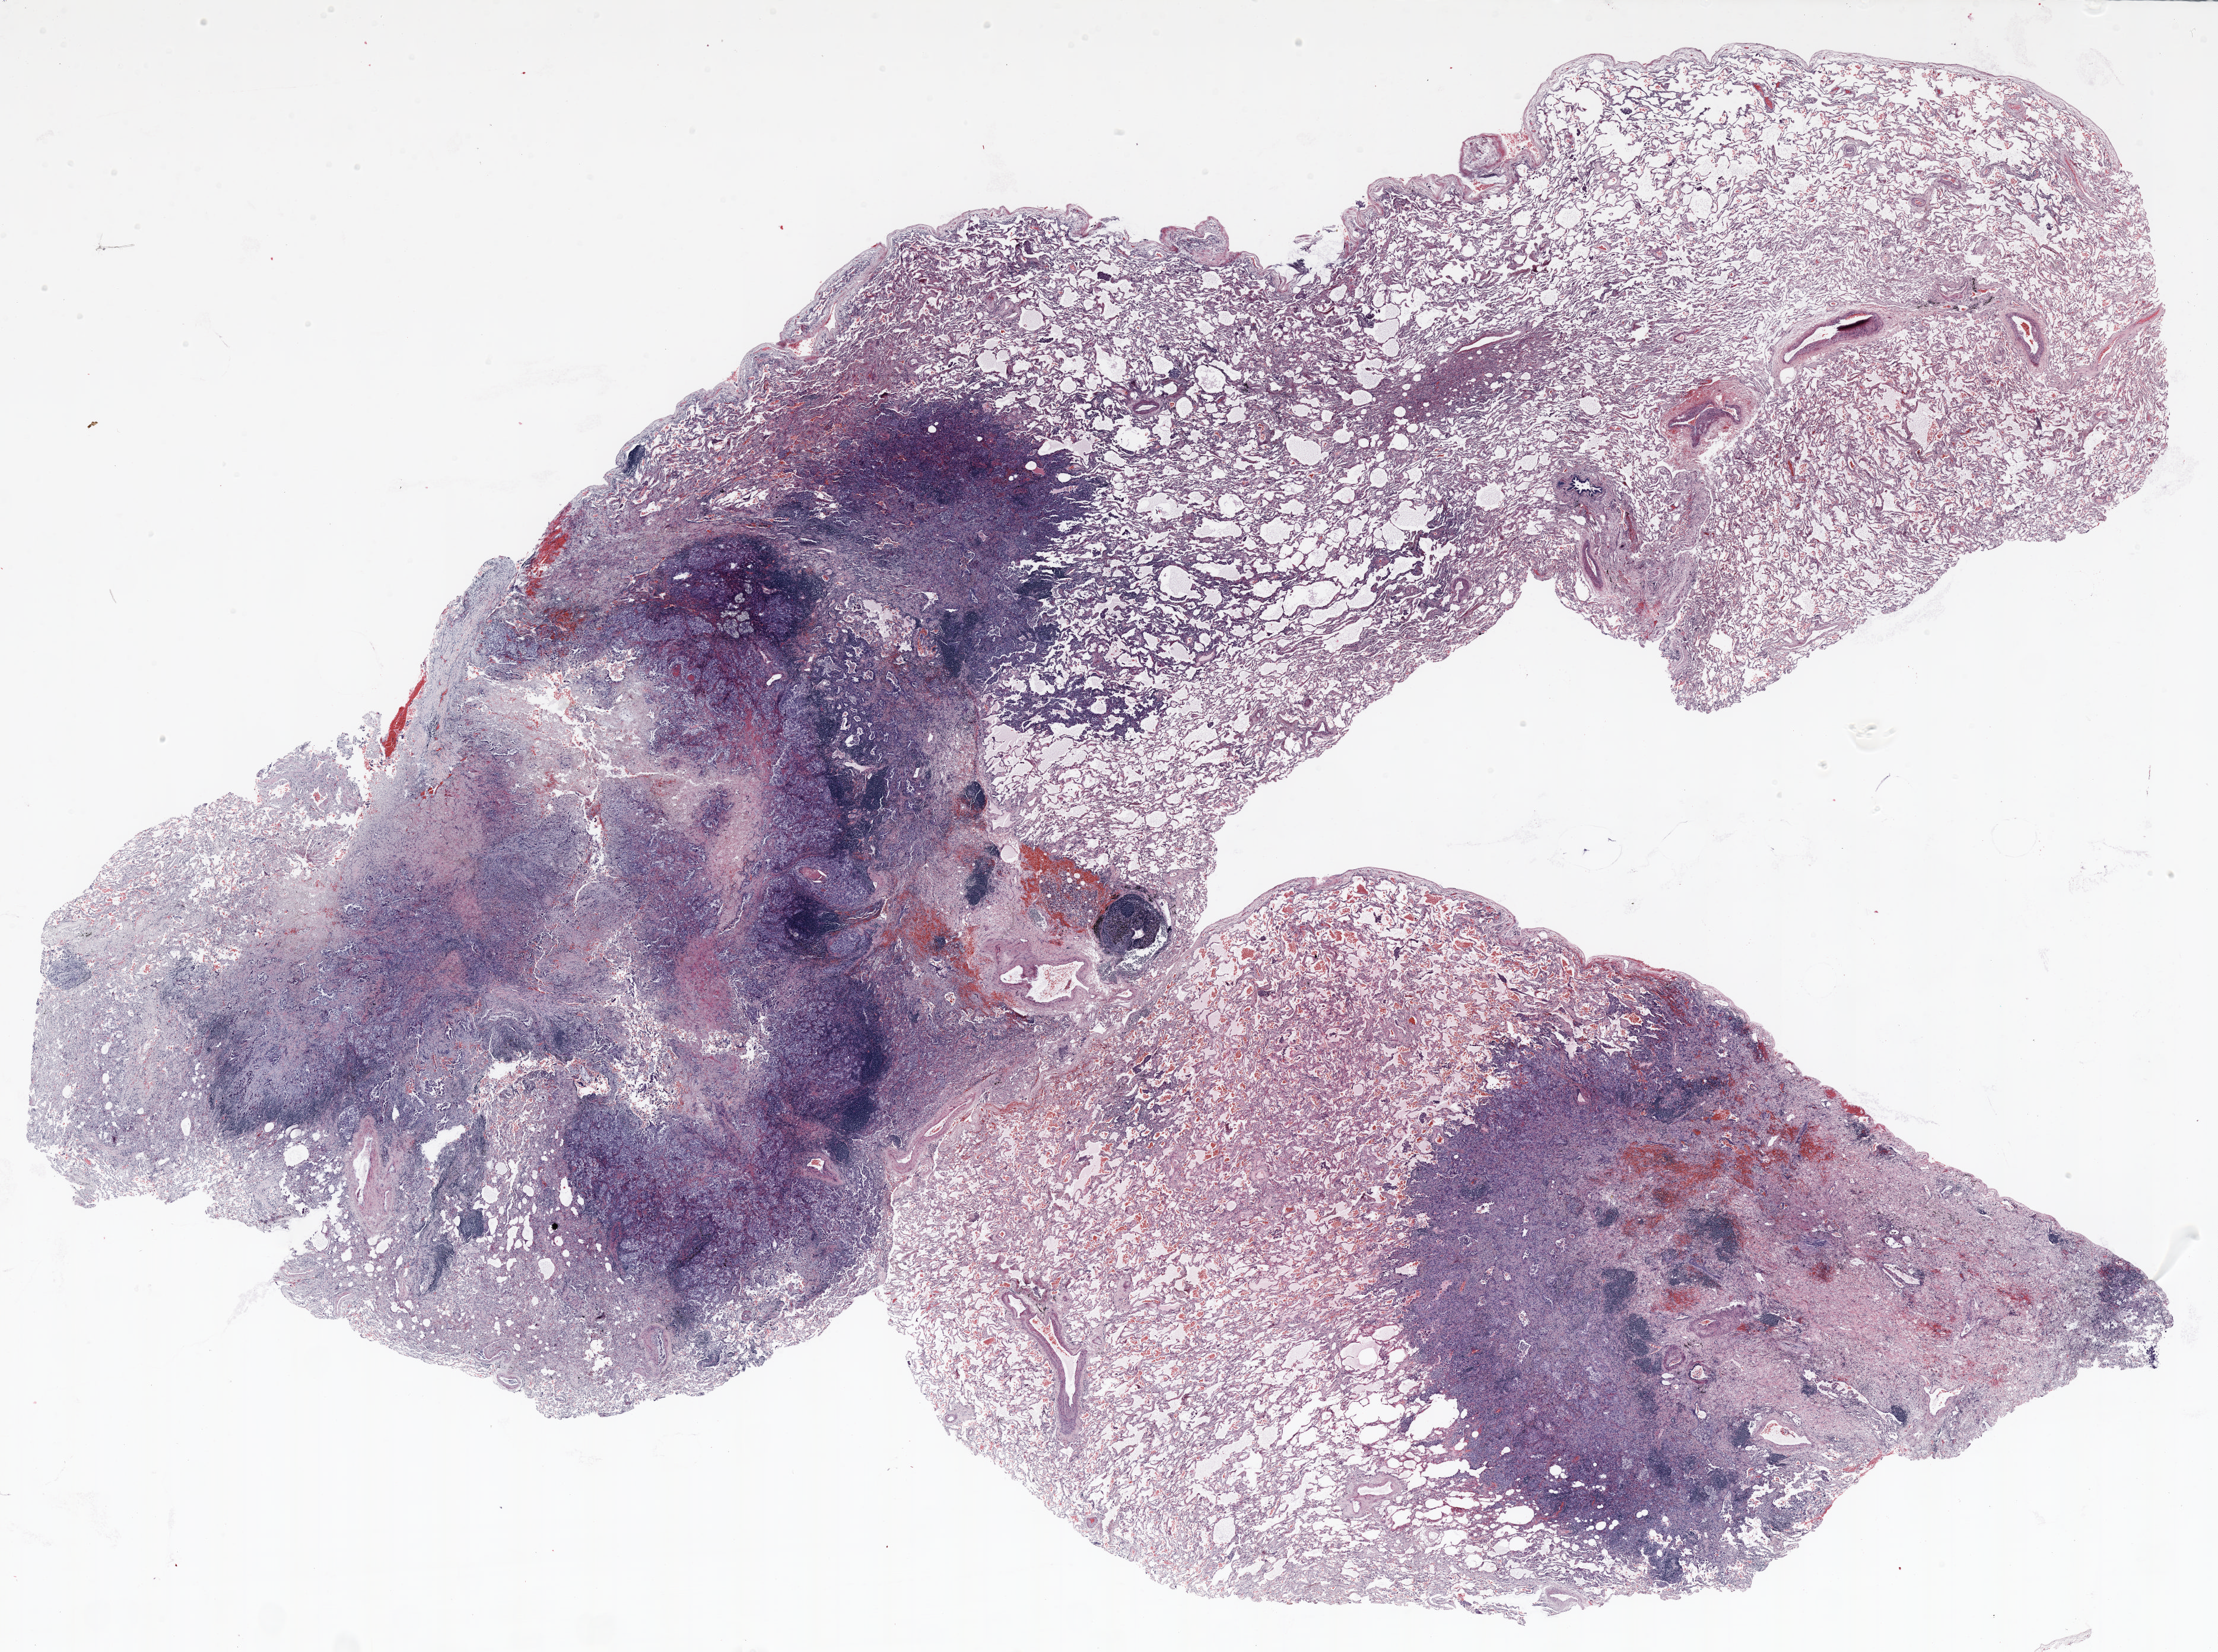
H&E-stained whole-slide image — shown as a low-resolution overview of the whole scanned area (about 30.0 x 22.4 mm). FFPE section. Lung. Female, age 67 at enrolment. Former smoker at enrolment. Grade: poorly differentiated (G3).
• tumour size (pathology): 30 mm
• participant's lung-cancer diagnosis: Adenocarcinoma with mixed subtypes (ICD-O-3 8255/3)
• stage (AJCC 6th edition): IA
• primary tumour location (clinical record): right upper lobe